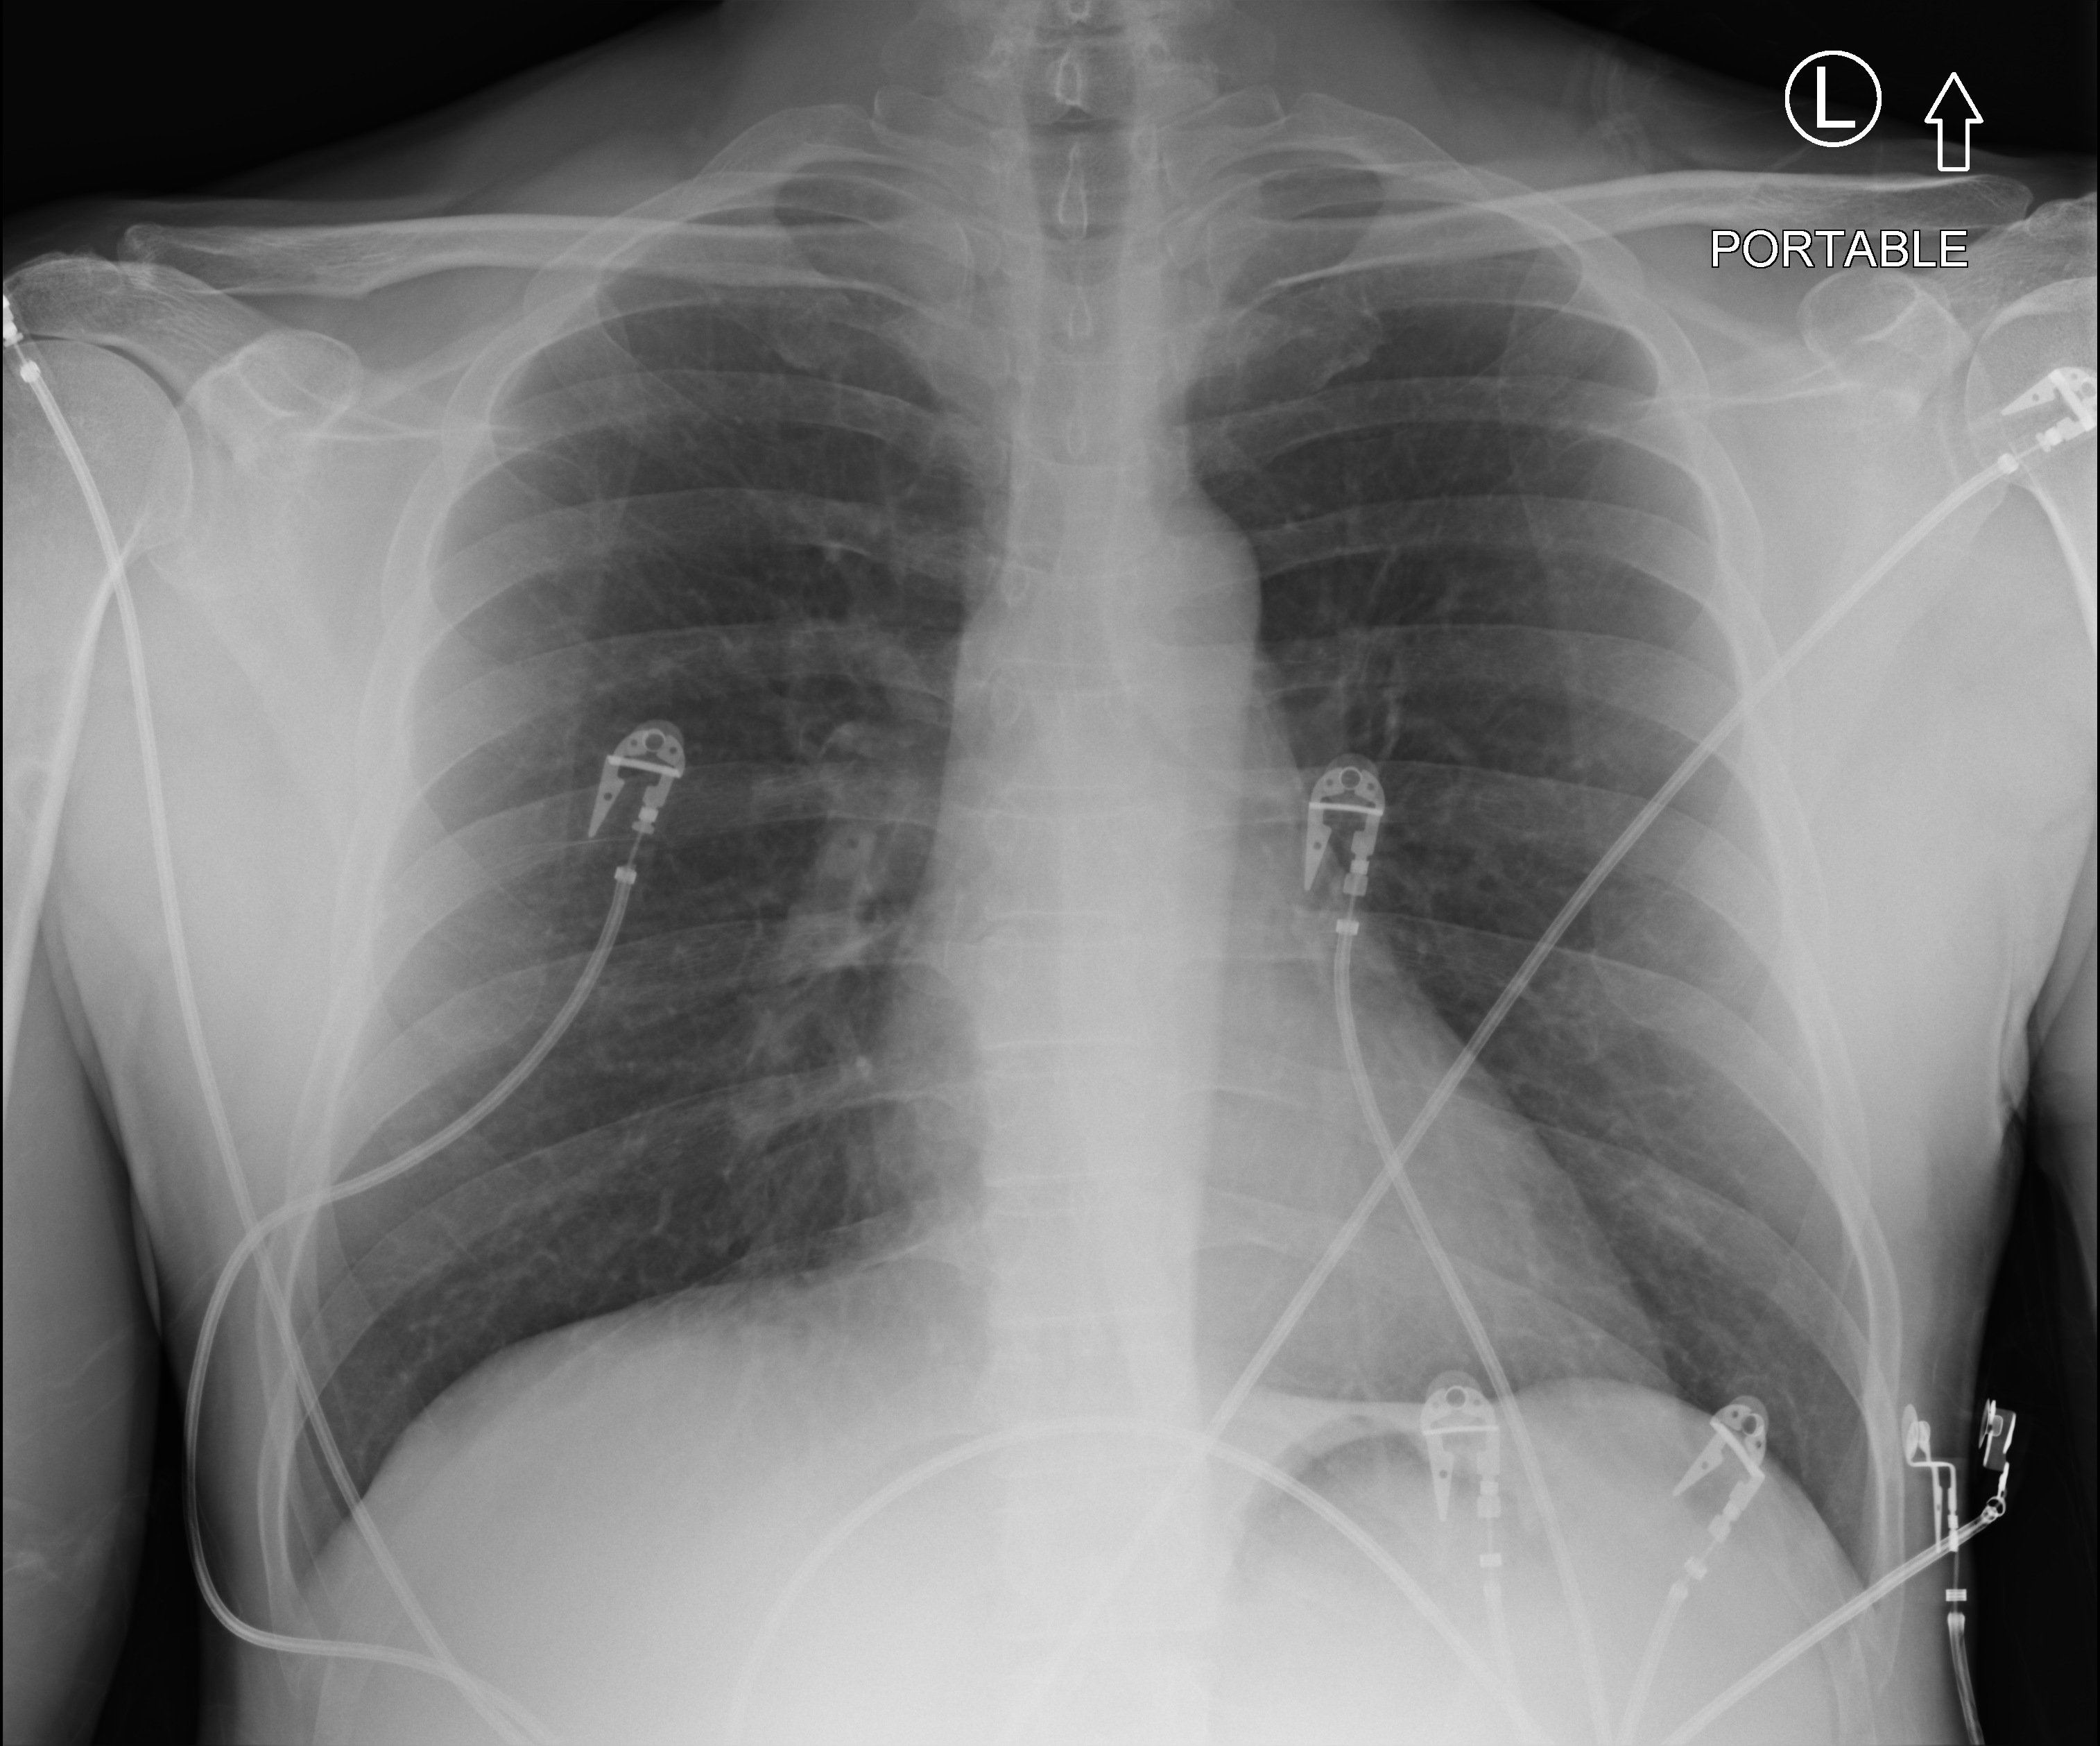
Portable chest radiograph; anteroposterior (AP) projection. Patient hospitalised with COVID-19; male, aged 18–59 years.
From the hospital-stay record, not from the radiograph (when in the stay this image was taken is not recorded):
- smoking status (admission record): never